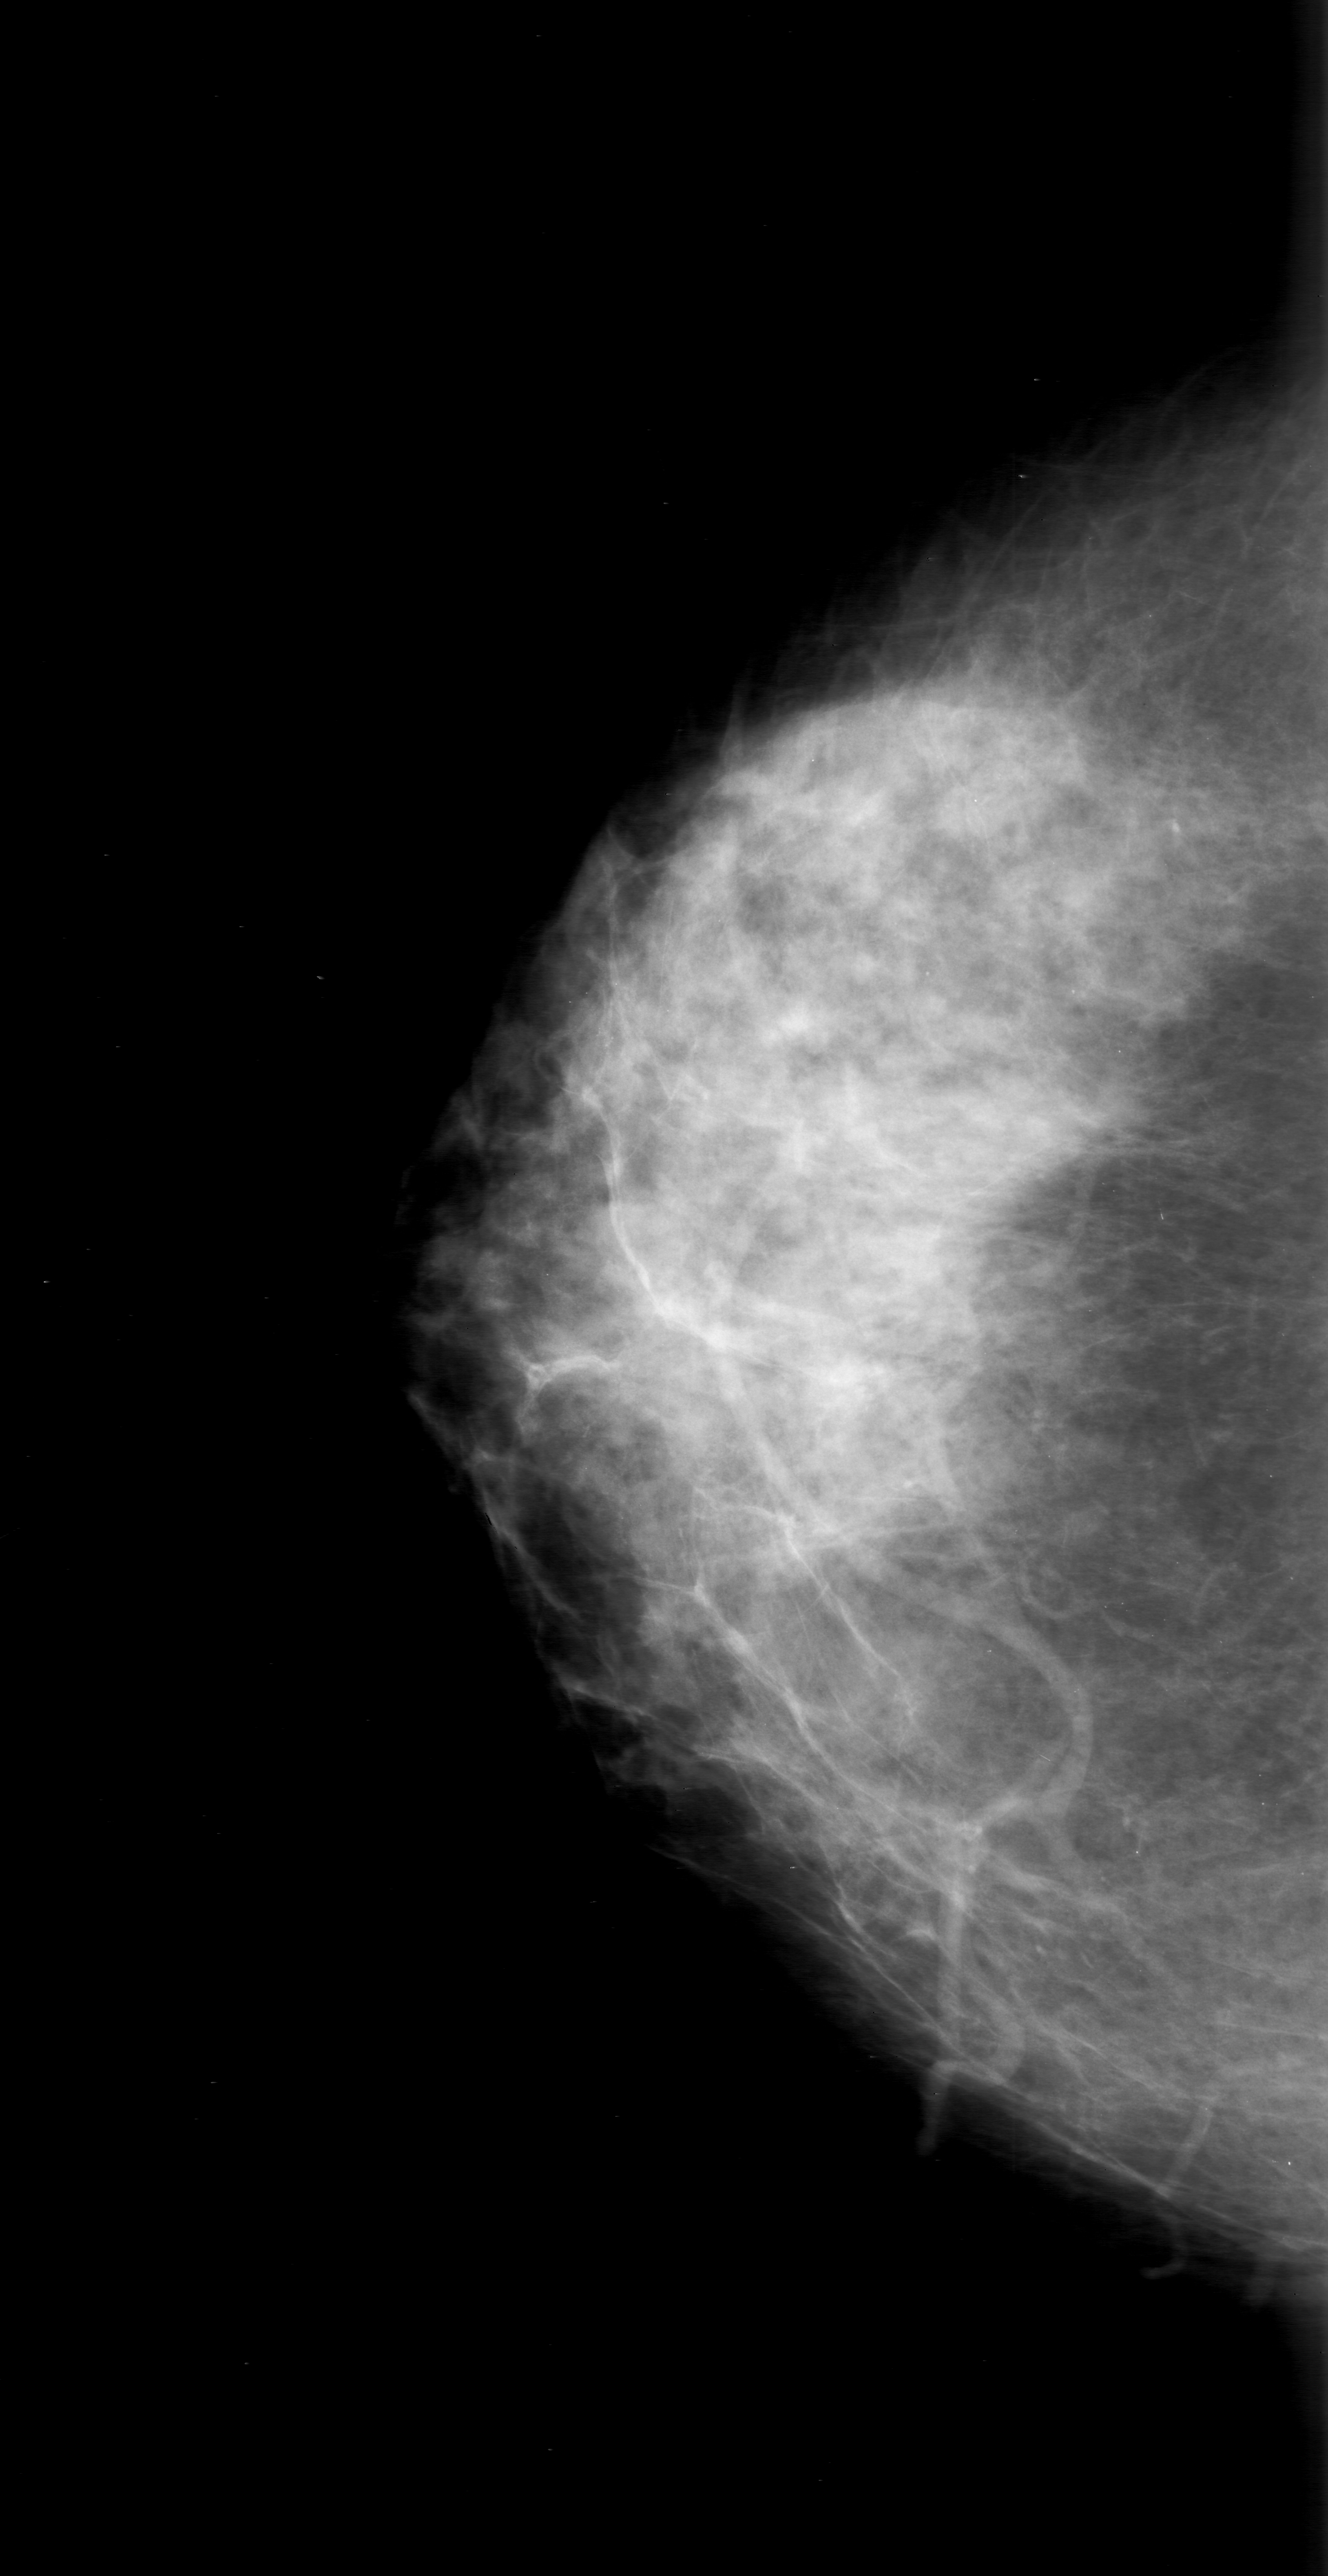
Mammogram (digitized film); right breast; craniocaudal (CC) view; BI-RADS breast density category 3 (scale 1–4).
Radiologist-marked abnormalities on this image: calcifications, morphology punctate, distribution clustered; BI-RADS assessment category 0 (incomplete: needs additional imaging); pathology result (as recorded, not read from the image): benign.